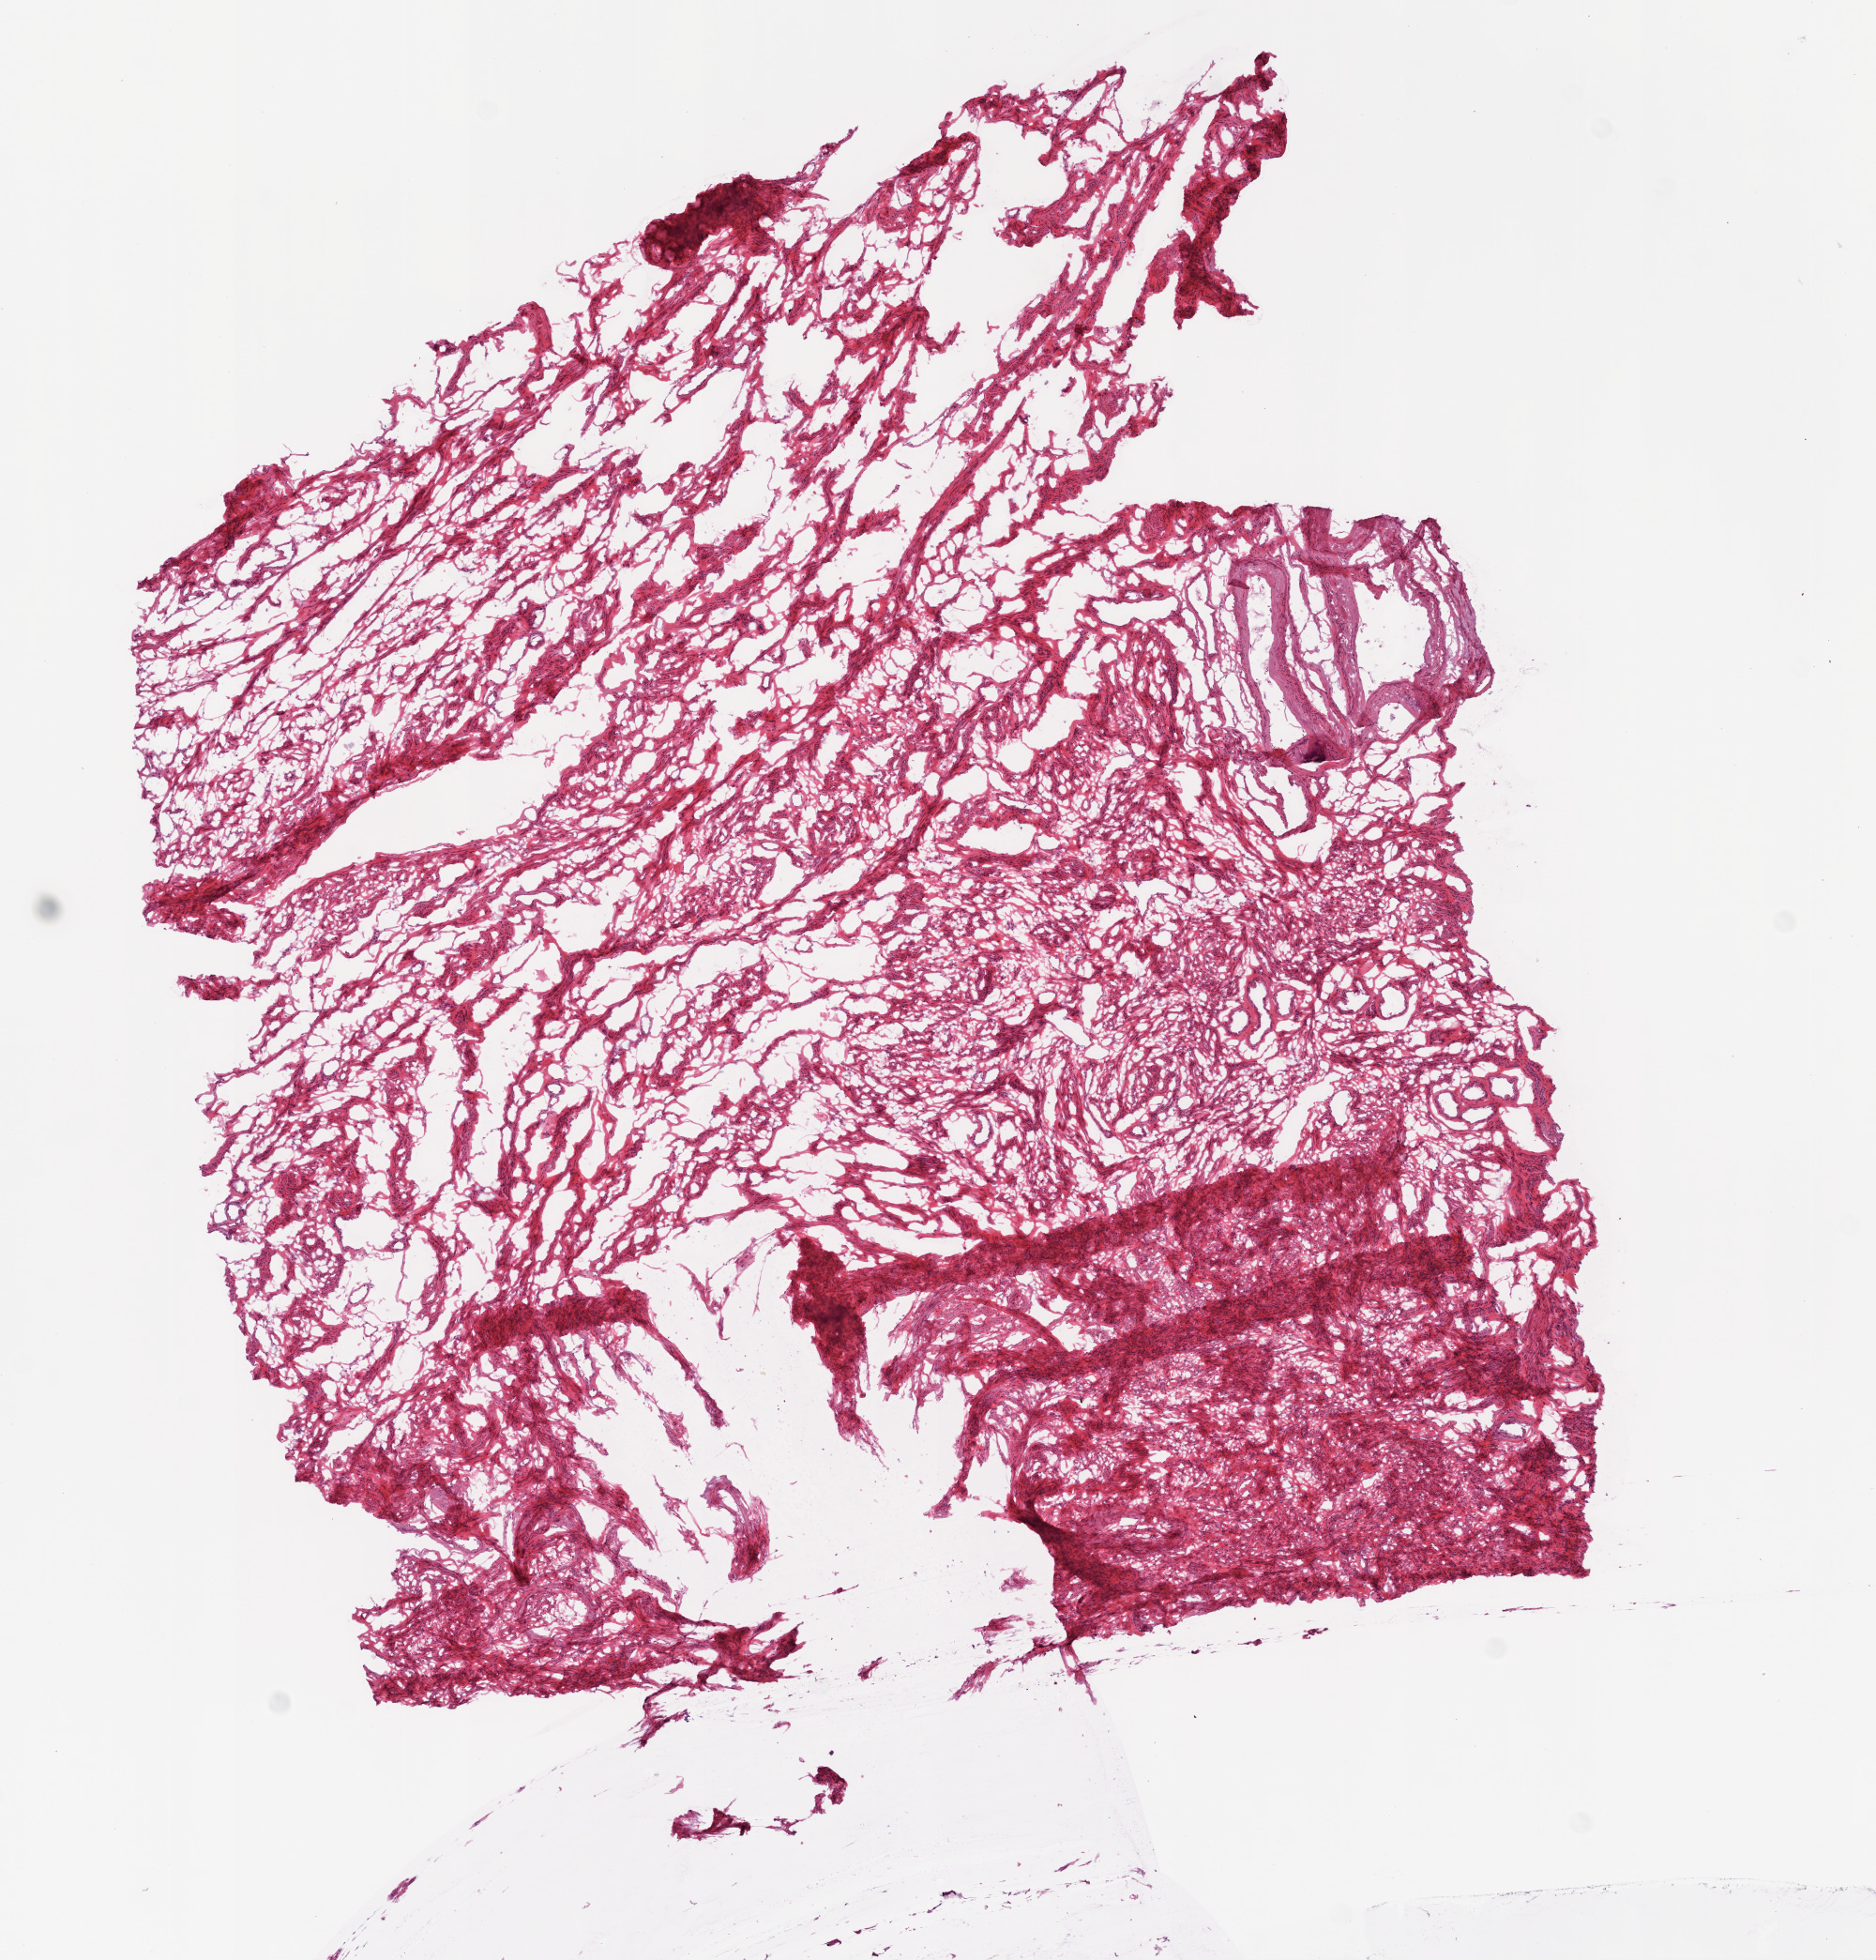
Whole-slide histology image, H&E-stained, shown as a low-resolution overview of the whole scanned area (about 8.0 x 8.4 mm), frozen section from the top of the tissue portion, sample: solid tissue normal (non-tumour tissue), ovary. Female, age 74 years at initial diagnosis.
This section: solid tissue normal (non-tumour) sample from the same patient. Patient diagnosis: Serous cystadenocarcinoma, NOS.